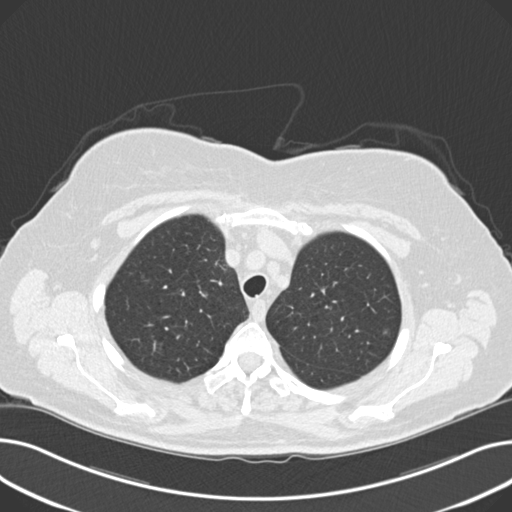
Low-dose screening chest CT, axial slice. Third screening round (two years after baseline). Lung window (W 1500 / L -600 HU). 2 mm slice thickness. Standard (soft-tissue) reconstruction kernel (B30f). Slice 46 of 203 in the series. 512 × 512 image matrix, field of view 372 × 372 mm. Female, age 60 years at enrolment.
Expert-annotated lung lesion, bounding box [x1, y1, x2, y2] px = [372, 317, 403, 352]. The screening reader recorded 8 non-calcified nodules or masses ≥4 mm on this exam (right upper lobe, lingula, lingula, right middle lobe, right lower lobe, left lower lobe, left lower lobe, left lower lobe); which of them this box marks is not recorded. Official screen result: positive, other. Lung cancer was diagnosed 176 days after this screen: non-small cell carcinoma, left upper lobe, poorly differentiated (G3), stage IB (AJCC 6th edition), 7 mm at pathology.